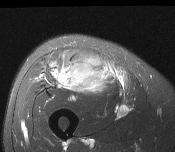
MRI of an extremity soft-tissue mass, one axial slice; slice 73 of 116 in the series (ordered by position); T2-weighted fat-saturated; MR volume resampled by the dataset authors to the PET/CT grid (not the native acquisition matrix); 3.27 mm slice thickness; 175 × 152 image matrix. Male patient. From the clinical record (not read from this slice): histological type: pleiomorphic leiomyosarcoma; grade: intermediate; site of the primary tumour: right thigh.
Annotated regions visible in this slice (expert contour drawn on MRI and transferred to this co-registered scan by the dataset authors):
- gross tumour volume including surrounding oedema: bounding box (x1, y1, x2, y2) in pixels: (53, 51, 109, 96)
- gross tumour volume (mass): (58, 54, 107, 94)